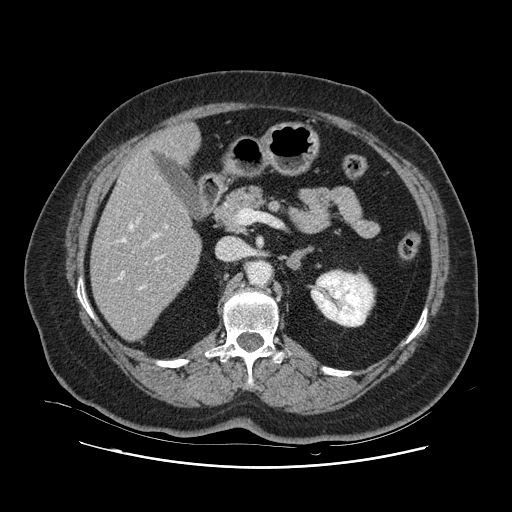
Contrast-enhanced abdominal CT, one axial slice. Intravenous contrast given. Soft-tissue window (W 400 / L 40 HU). 2.5 mm slice thickness. 512 × 512 image matrix, field of view 391 × 391 mm. Female patient, age 73 years. From the clinical record (not read from this slice): diagnosis: colorectal cancer liver metastases, imaged before liver resection; multiple liver metastases: no; largest metastasis: 7 cm; disease in both lobes: no.
Annotated regions visible in this slice (outlined manually by an expert reader):
- hepatic veins: bounding box (x1, y1, x2, y2) in pixels: (118, 218, 169, 320)
- liver: (92, 125, 201, 340)
- planned liver remnant (the part of the liver to remain after resection): (92, 147, 201, 340)
- portal vein (with intrahepatic branches): (138, 225, 168, 290)